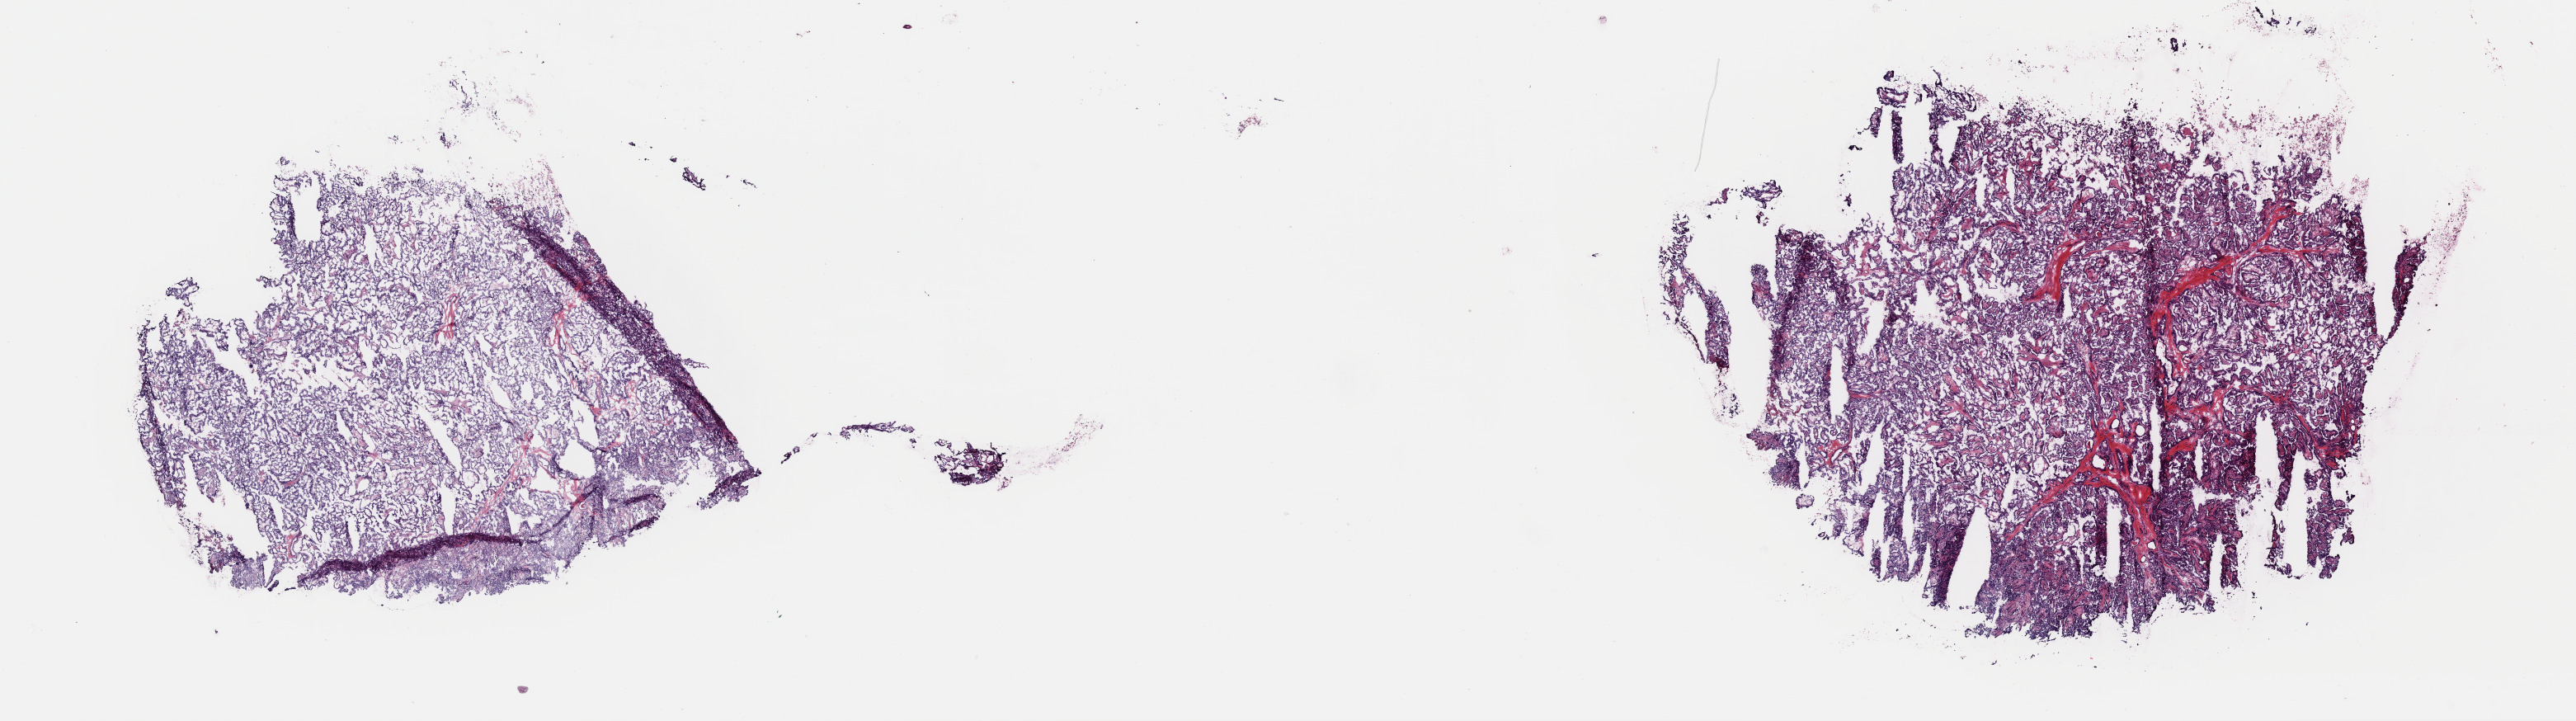
Whole-slide histology image, H&E, whole scanned area (about 24.7 x 6.9 mm, slide scanned at 40x) shown as a low-resolution overview, frozen section, thyroid, primary tumour sample. Female, age 39 years at initial diagnosis. Pathologist review of this section (percent, as recorded): tumour cells 95%, tumour nuclei 80%, normal cells 0%, stromal cells 5%, necrosis 0%. Inflammatory infiltration, as recorded: lymphocyte infiltration 1%, monocyte infiltration 1%, neutrophil infiltration 0%.
- laterality: left
- TNM: T1a N1a M0
- AJCC pathologic stage: I (7th edition)
- pathologic diagnosis: Papillary carcinoma, columnar cell (thyroid gland)